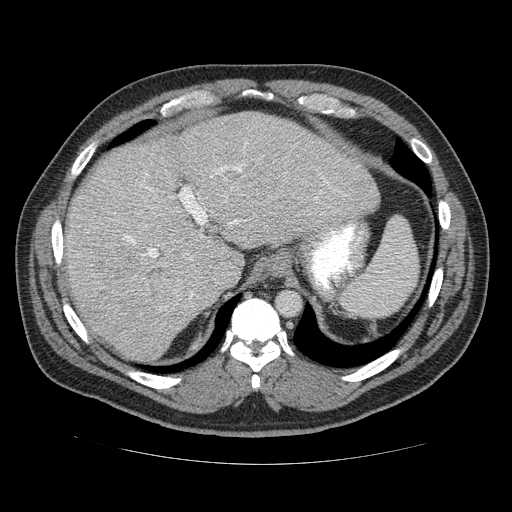
Contrast-enhanced abdominal CT (liver protocol), one axial slice; slice 95 of 113 in the series (ordered by position); 120 kVp; soft-tissue window (W 400 / L 40 HU); 512 × 512 image matrix, field of view 400 × 400 mm. From the clinical record (not read from this slice): diagnosis: hepatocellular carcinoma (patient treated with transarterial chemoembolisation; whether this scan precedes or follows treatment is not stated here); TNM stage (as recorded): Stage-II; Child-Pugh class: B; tumour differentiation: moderately differentiated; tumour nodularity: multinodular.
Structures marked on this image (semi-automatic segmentation, software-assisted and operator-edited):
- abdominal aorta: bounding box <277,291,301,316> (left, top, right, bottom; pixels)
- liver parenchyma outside the tumour (the mass and vessels are separate outlines, so this box may not span the whole liver): <60,112,380,359>
- mass: <95,241,179,310>
- liver vessels: <125,173,268,296>